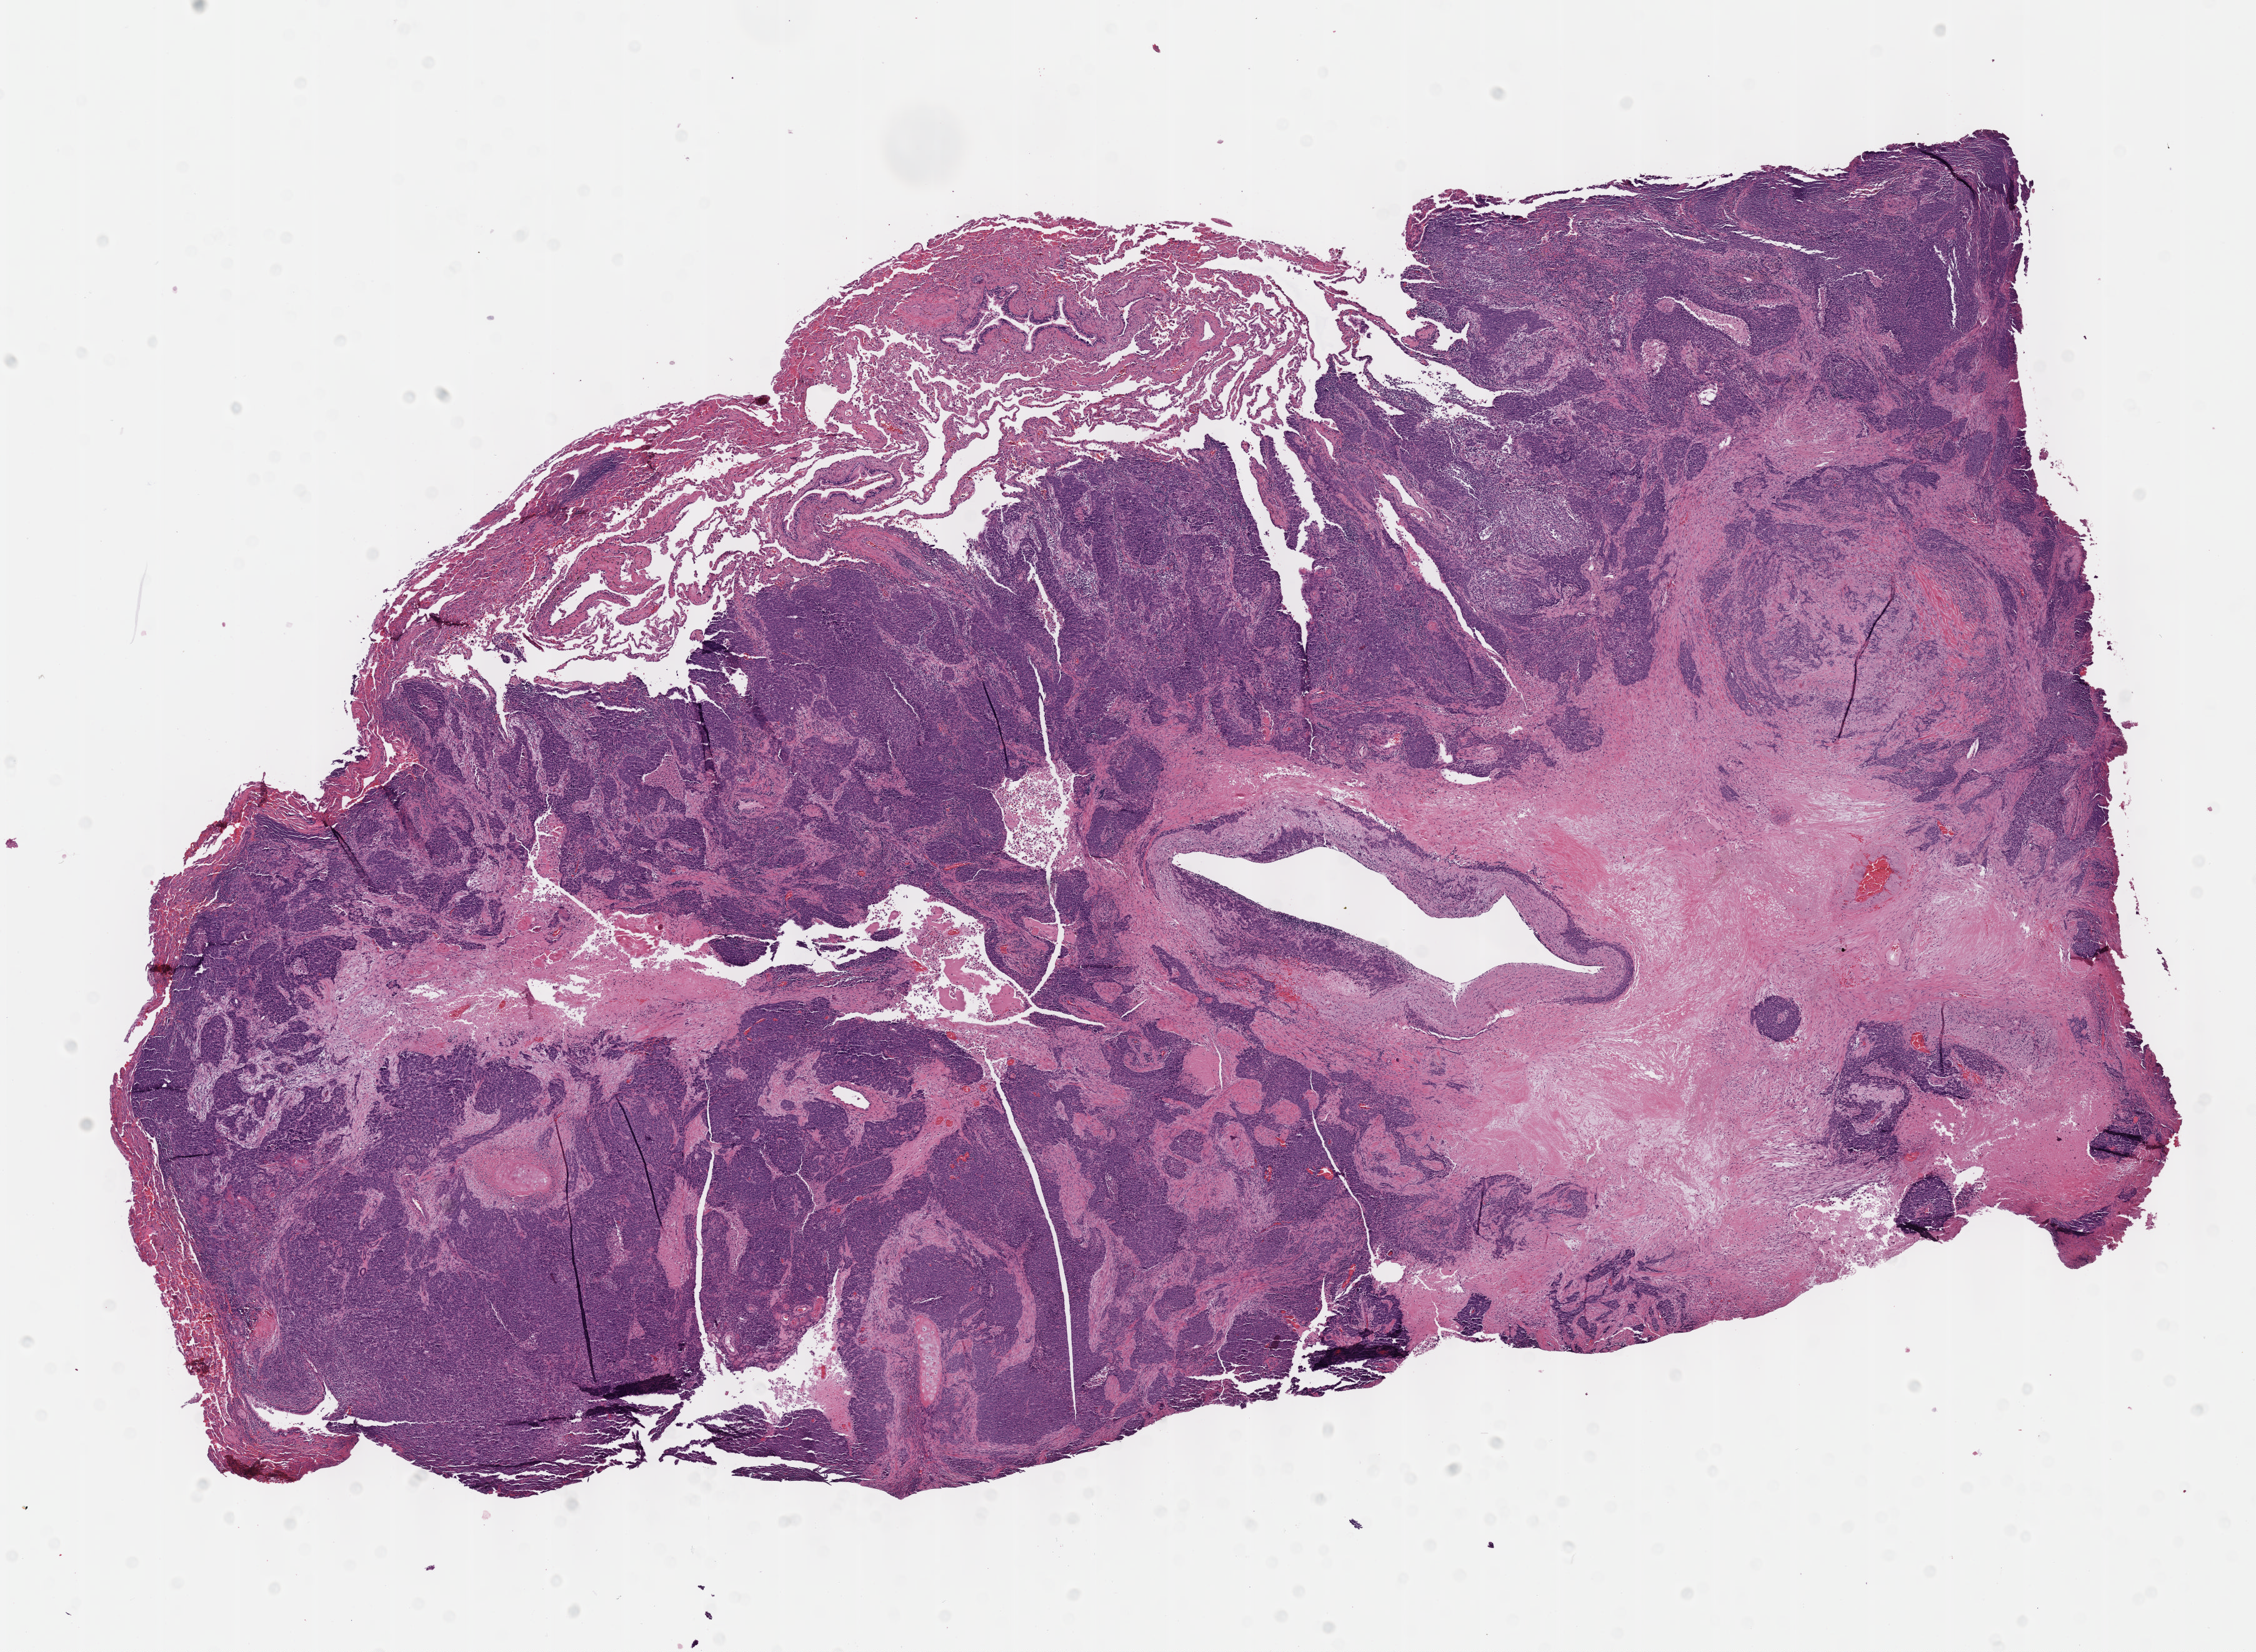
Whole-slide histology image, H&E — whole scanned area (about 14.6 x 10.7 mm) shown as a low-resolution overview, formalin-fixed paraffin-embedded (FFPE) diagnostic section, lung, primary tumour sample. Female patient; age at initial diagnosis 66 years.
- pathologic diagnosis: Squamous cell carcinoma, NOS (upper lobe, lung)
- AJCC pathologic stage: IA
- TNM: T1b N0 M0